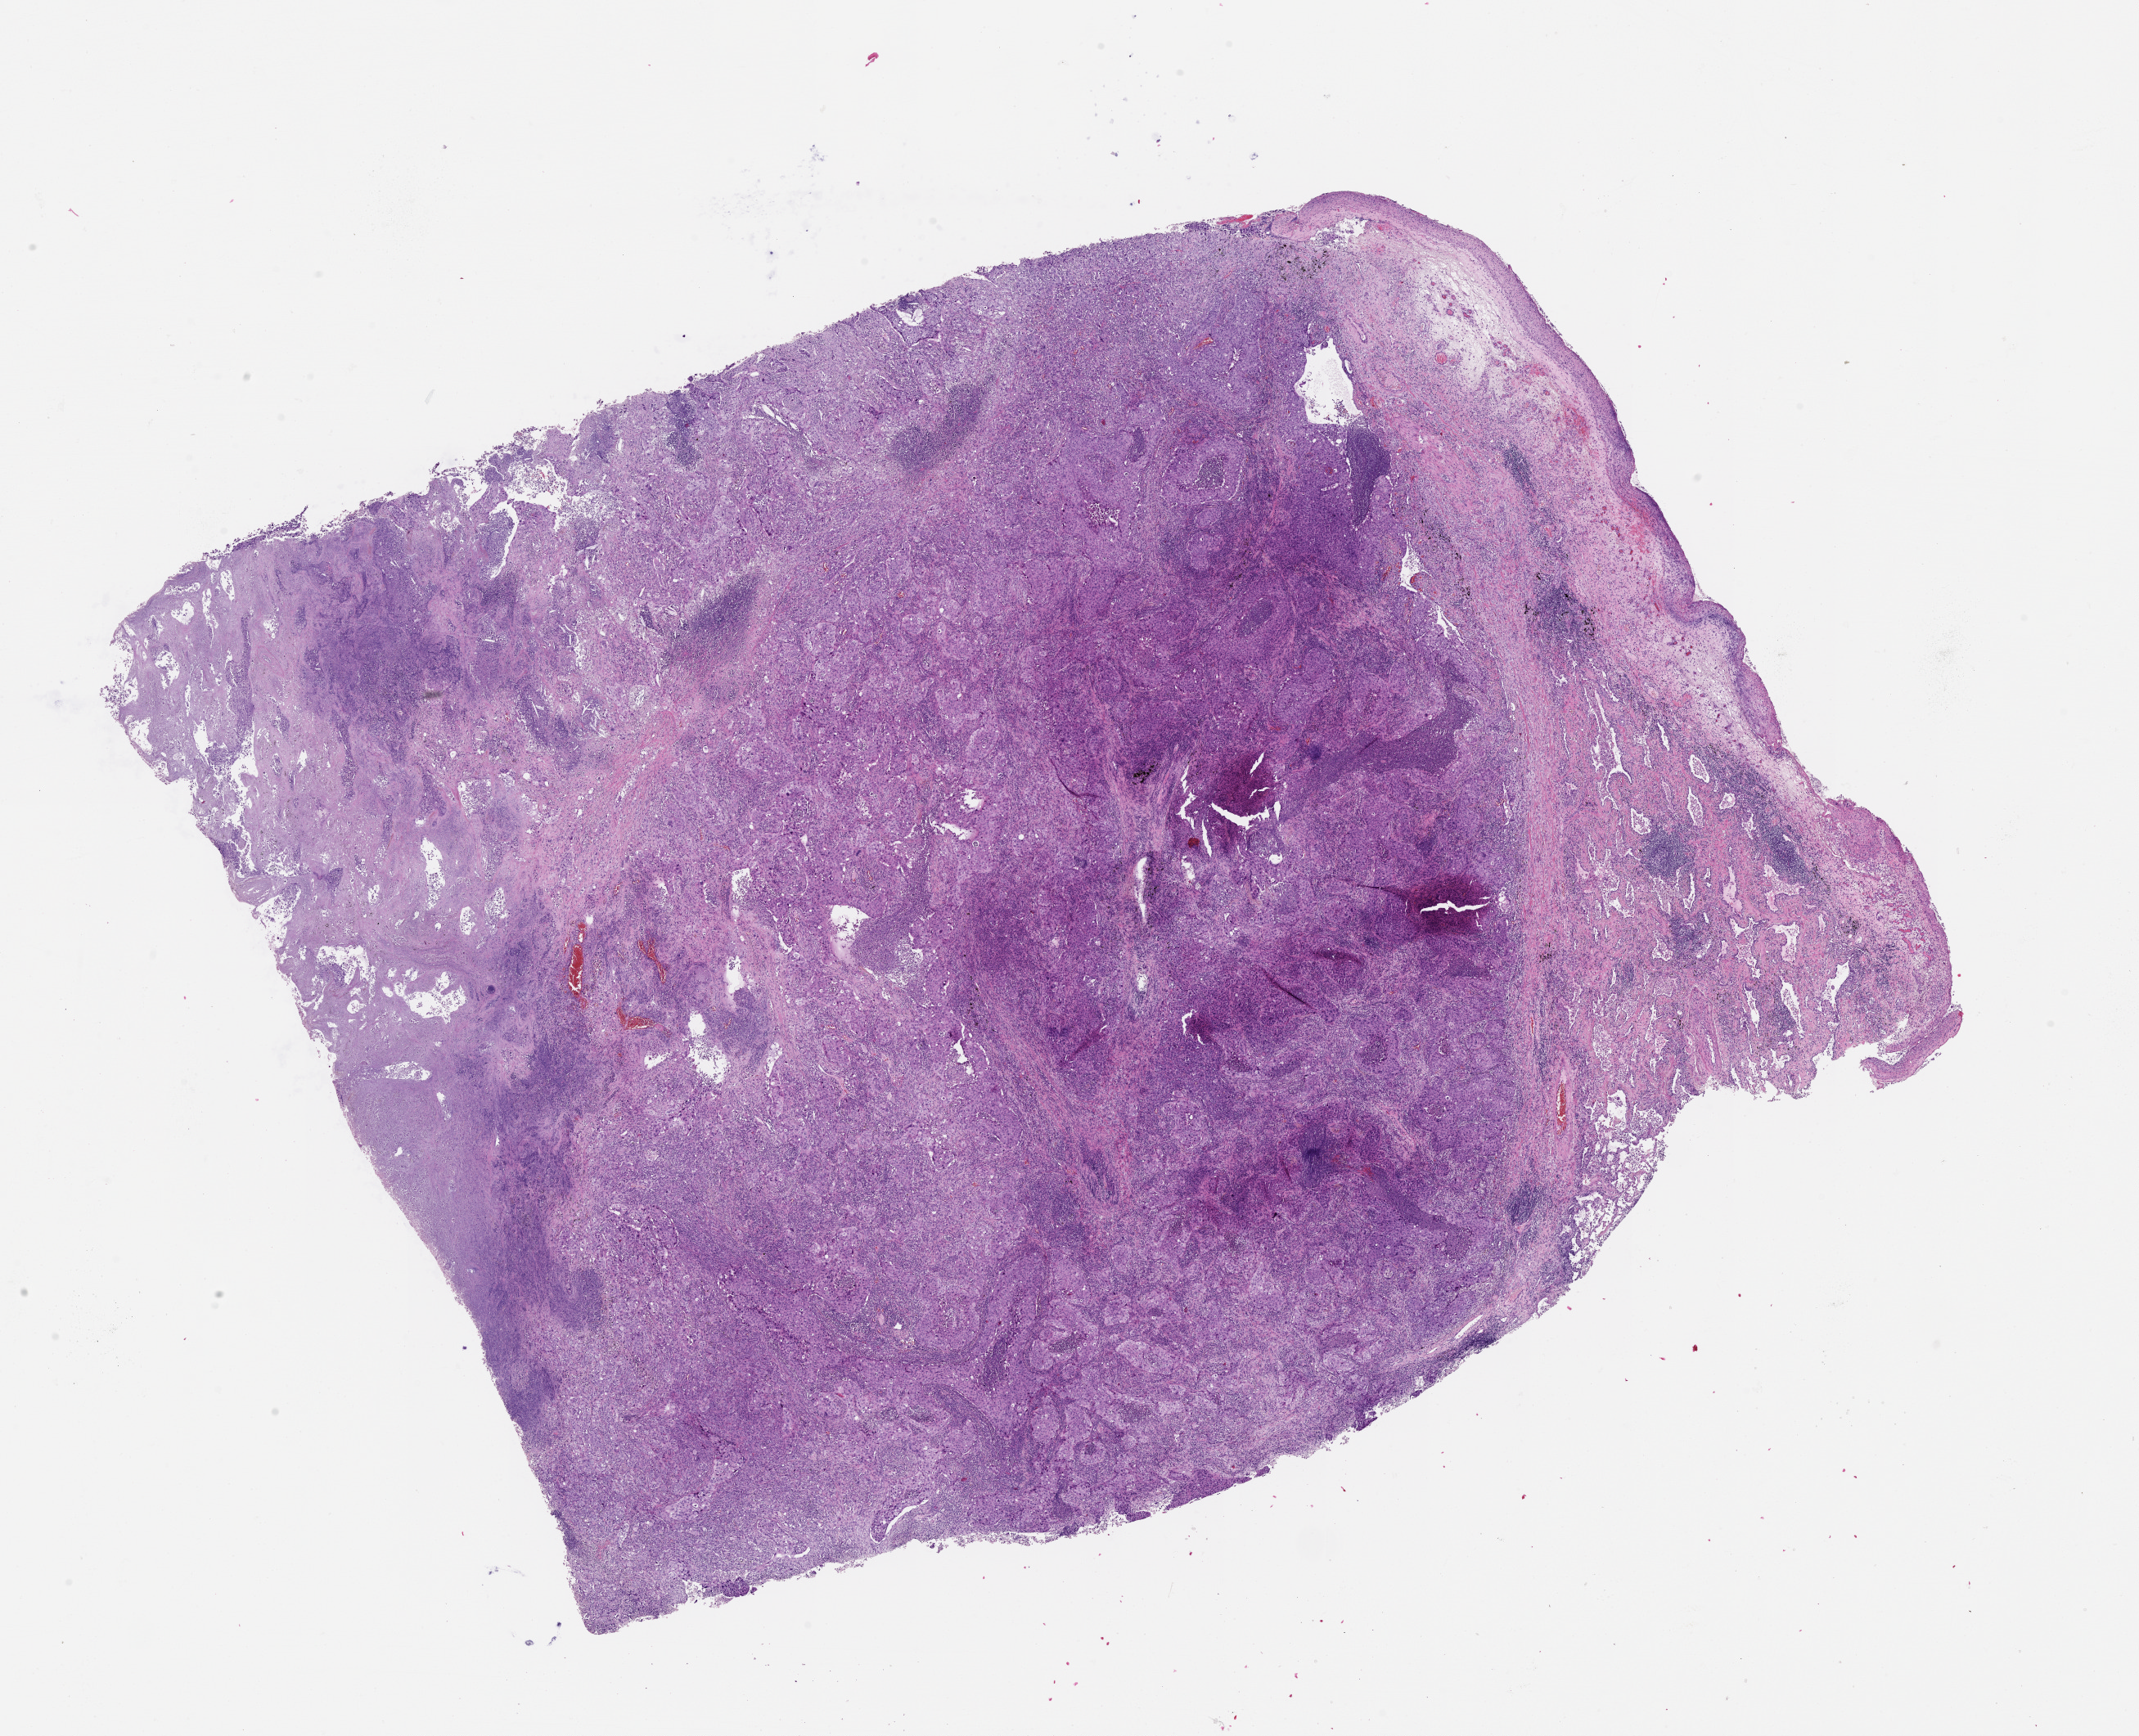
Whole-slide histology image, H&E-stained — shown as a low-resolution overview of the whole scanned area (about 21.0 x 17.1 mm), lung, tissue type not recorded.
Patient diagnosis (cohort enrolment): squamous cell carcinoma (lung).